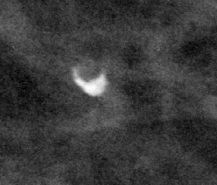
Crop from a digitized film mammogram around one marked abnormality; left breast; MLO view.
Calcifications, morphology lucent center; BI-RADS assessment category 2; subtlety rating 5 on a 1 (subtle) to 5 (obvious) scale; benign; no additional work-up was recommended (benign without callback).